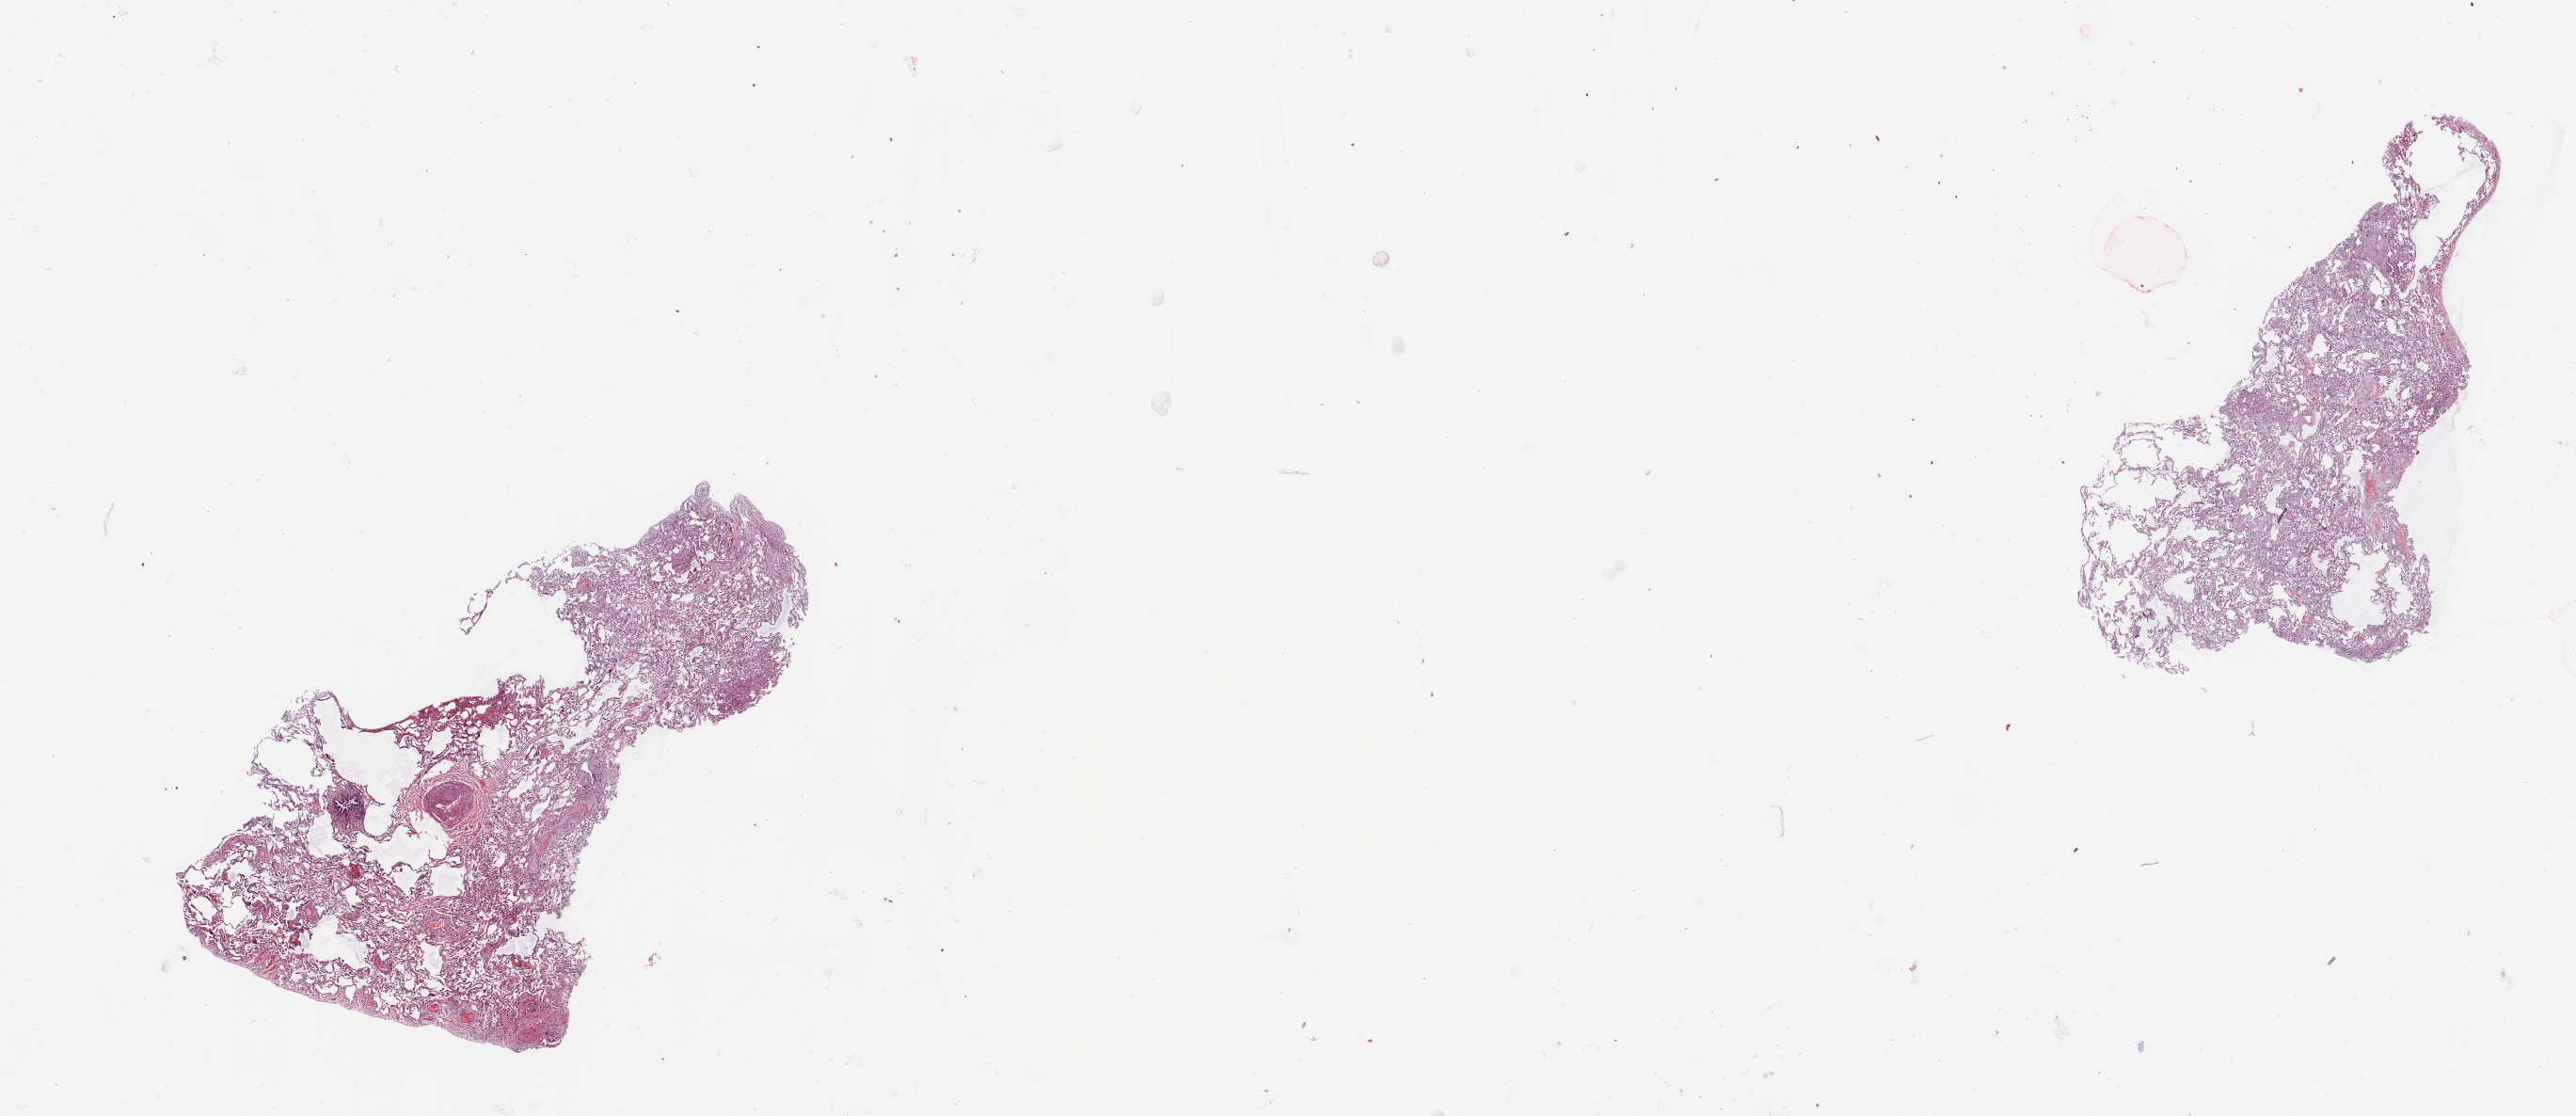
H&E whole-slide image, low-resolution overview of the scanned area, about 21.7 x 9.4 mm (slide scanned at 20x). Normal (non-tumour) tissue sample, sampled site: lung. Patient: female, age 70 years.
* this section: normal (non-tumour) tissue from the same patient
* patient diagnosis: Adenocarcinoma, NOS